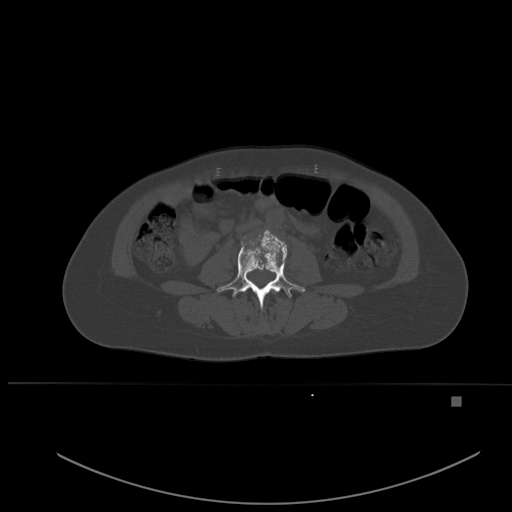
CT including the spine, one axial slice. Position 194 of 651 along the scan axis. Bone window (W 1800 / L 400 HU). 1.5 mm slice thickness. 512 × 512 image matrix, field of view 443 × 443 mm. Patient: female, 49 years. Case-level facts recorded for this patient, not image findings: primary cancer: breast; vertebrae with lytic lesions (as recorded): L3, T12, L4.
Outlined on this slice (semi-automatically segmented with operator editing):
- L3 vertebra: bounding box (x1, y1, x2, y2) in pixels: (217, 231, 305, 309)